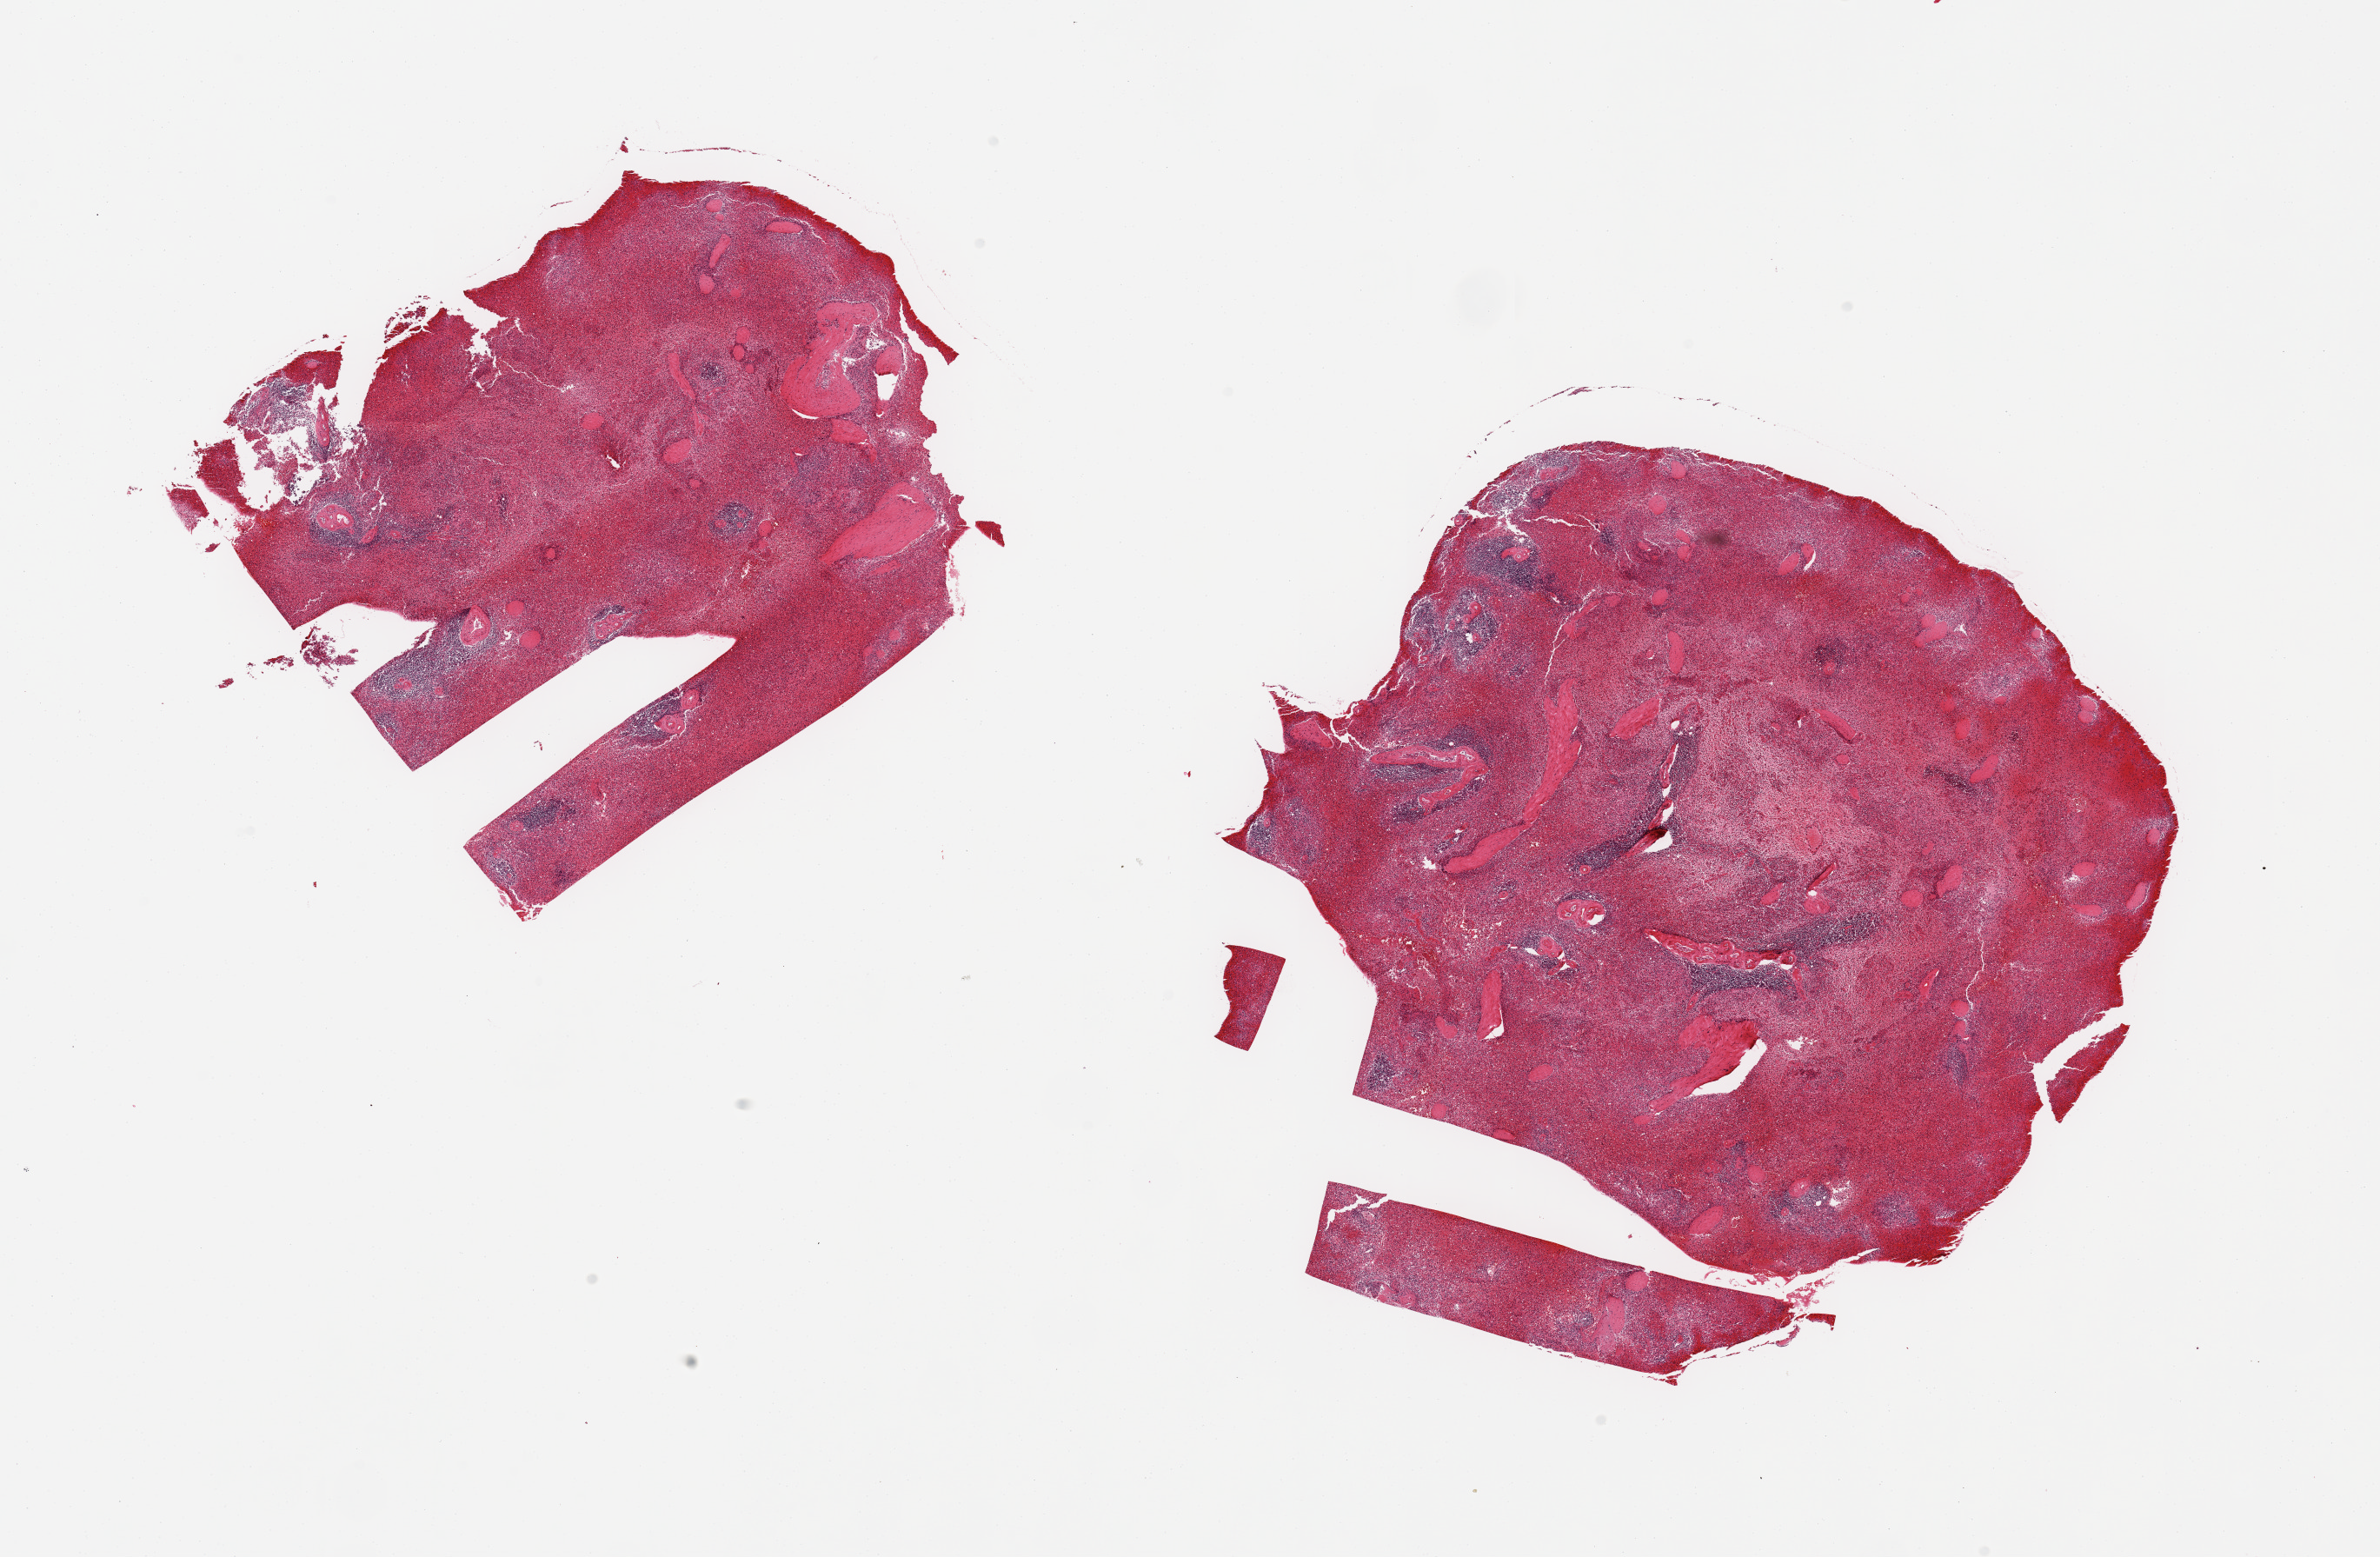
Whole-slide image, haematoxylin and eosin stain, brightfield, low-resolution overview of the scanned area, about 21.7 x 14.2 mm. PAXgene-fixed paraffin-embedded (PFPE) section. Sampled site (target tissue): spleen. Tissue donor sample.
Reviewer comment on this tissue sample: 2 pieces marked congestion.